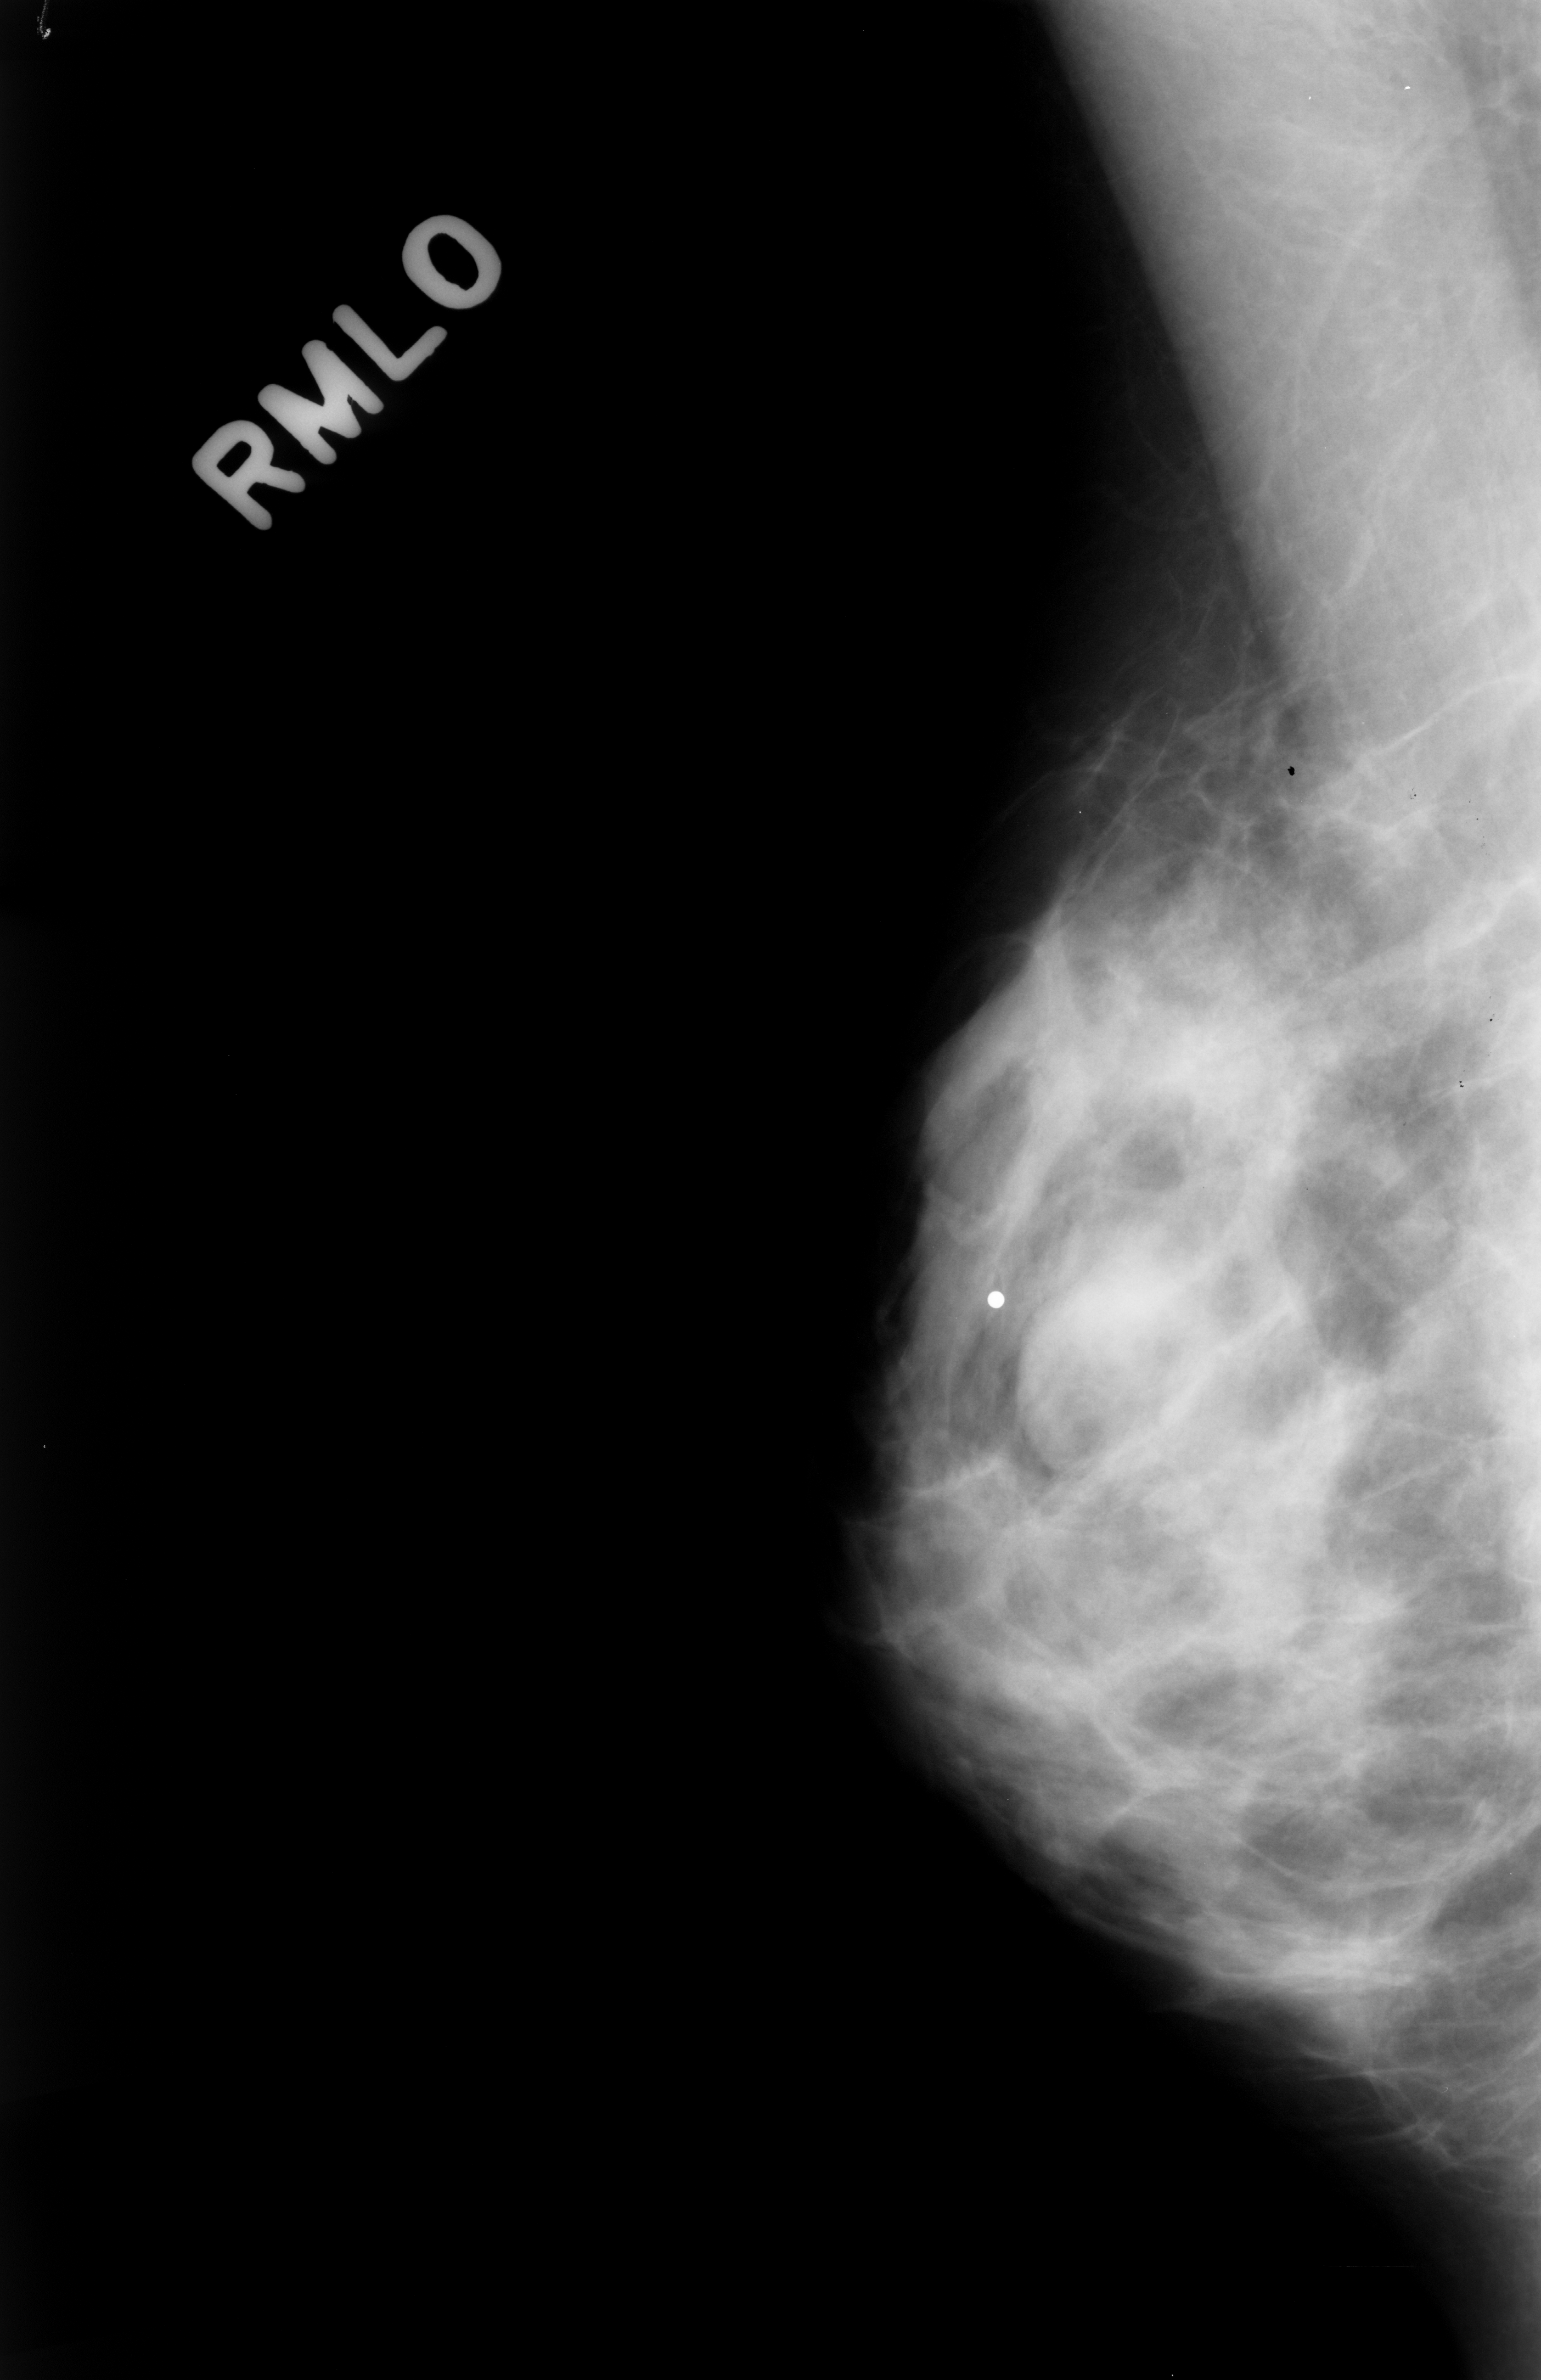
Mammogram (digitized film). Right breast. MLO view. 1541 × 2380 image matrix.
Expert-marked regions of interest on this image (one box per marked abnormality):
- mass, shape oval, margins obscured; BI-RADS assessment category 3; subtlety rating 4 on a 1 (subtle) to 5 (obvious) scale; pathology (as recorded): benign: bounding box [x1, y1, x2, y2] px = [980, 1225, 1177, 1495]